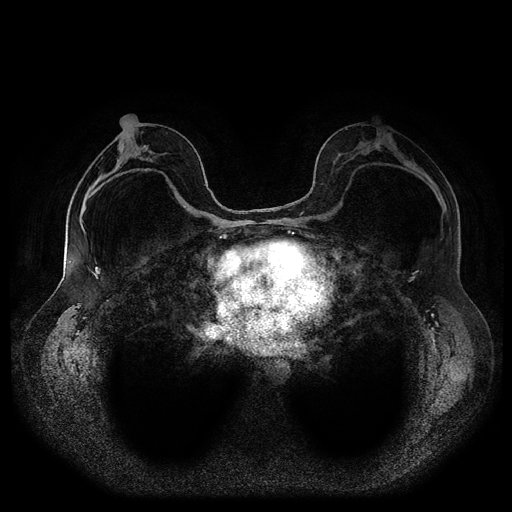
Breast MRI (dynamic contrast-enhanced, multi-phase), one axial slice; position 52 of 116 along the scan axis; dynamic contrast-enhanced series, time point 2 of 5 at this slice position (early post-contrast); 1.5 T; TE 2.6 ms, TR 5.3 ms; 512 × 512 image matrix. Patient: female, 46 years.
Outlined on this slice (semi-automatically segmented with operator editing):
- breast lesion (labelled 'tumour' in the annotation; benign lesions carry a separate 'benign' label): bounding box (x1, y1, x2, y2) in pixels: (119, 143, 123, 150)